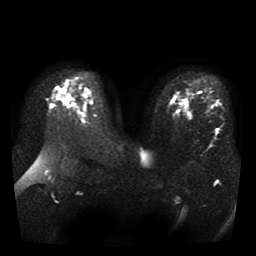
Breast MRI, one axial slice. Slice 29 of 41 in the series (ordered by position). Diffusion-weighted series; image 2 of 4 stored at this slice position (different b-values; order by instance number). 1.5 T. 5 mm slice thickness. 256 × 256 image matrix. Female patient.
Outlined on this slice (manually delineated by an expert):
- tumour on diffusion-weighted imaging: bounding box [x1, y1, x2, y2] px = [186, 113, 192, 118]